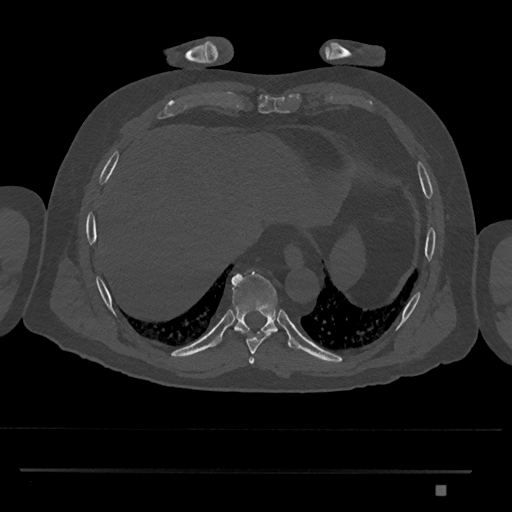
CT including the spine, one axial slice; position 1080 of 1134 along the scan axis; reconstruction kernel Br40s/3; 120 kVp; bone window (W 1800 / L 400 HU); 512 × 512 image matrix. Patient: male, 65 years. Case-level facts recorded for this patient, not image findings: primary cancer: prostate.
Annotated regions visible in this slice (semi-automatically segmented with operator editing):
- T8 vertebra: bounding box [x1, y1, x2, y2] px = [234, 330, 275, 354]
- T9 vertebra: [232, 269, 278, 334]